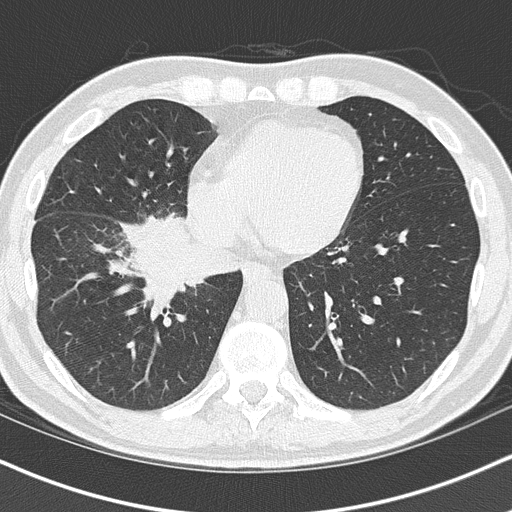
Axial slice from a low-dose chest CT screening exam, baseline screening round, lung window (W 1500 / L -600 HU). Male, age 55 years at enrolment. Current smoker at enrolment.
Lesion marked by an expert reader, bounding box (x1, y1, x2, y2) in pixels: (124, 223, 243, 313). Screening reader's record for this exam (one nodule recorded; not confirmed to be the boxed lesion): non-calcified nodule or mass ≥4 mm, right lower lobe, 6 × 5 mm, spiculated (stellate) margins, soft tissue attenuation. Participant outcome: lung cancer diagnosed 21 days after this screen — carcinoma, NOS, right hilum, stage IB (AJCC 6th edition), 67 mm at pathology.